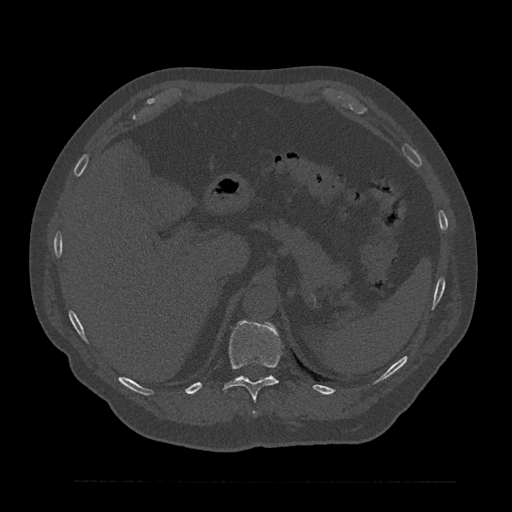
CT including the spine, one axial slice; slice 286 of 797 in the series (ordered by position); 120 kVp; bone window (W 1800 / L 400 HU); 0.5 mm slice thickness; 512 × 512 image matrix, field of view 430 × 430 mm. Male patient, age 61 years. From the clinical record (not read from this slice): primary cancer: prostate.
Structures marked on this image (semi-automatic segmentation, software-assisted and operator-edited):
- T11 vertebra: box from (x=222, y=320) to (x=281, y=401) px